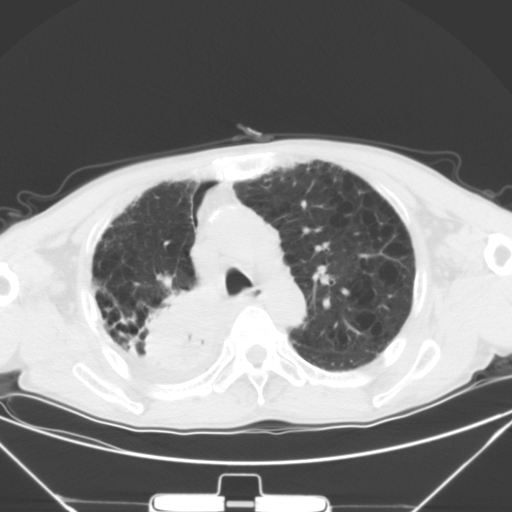
Chest CT, one axial slice. Position 34 of 50 along the scan axis. Lung window (W 1500 / L -600 HU). 5 mm slice thickness. 512 × 512 image matrix. Patient: male, 65 years. Case-level facts recorded for this patient, not image findings: clinical TNM (as recorded): T3 N1 M1a.
Annotated regions visible in this slice (rectangle marked by the reading radiologist):
- lung tumour (recorded histology: squamous cell carcinoma): bounding box (x1, y1, x2, y2) in pixels: (137, 274, 241, 402)